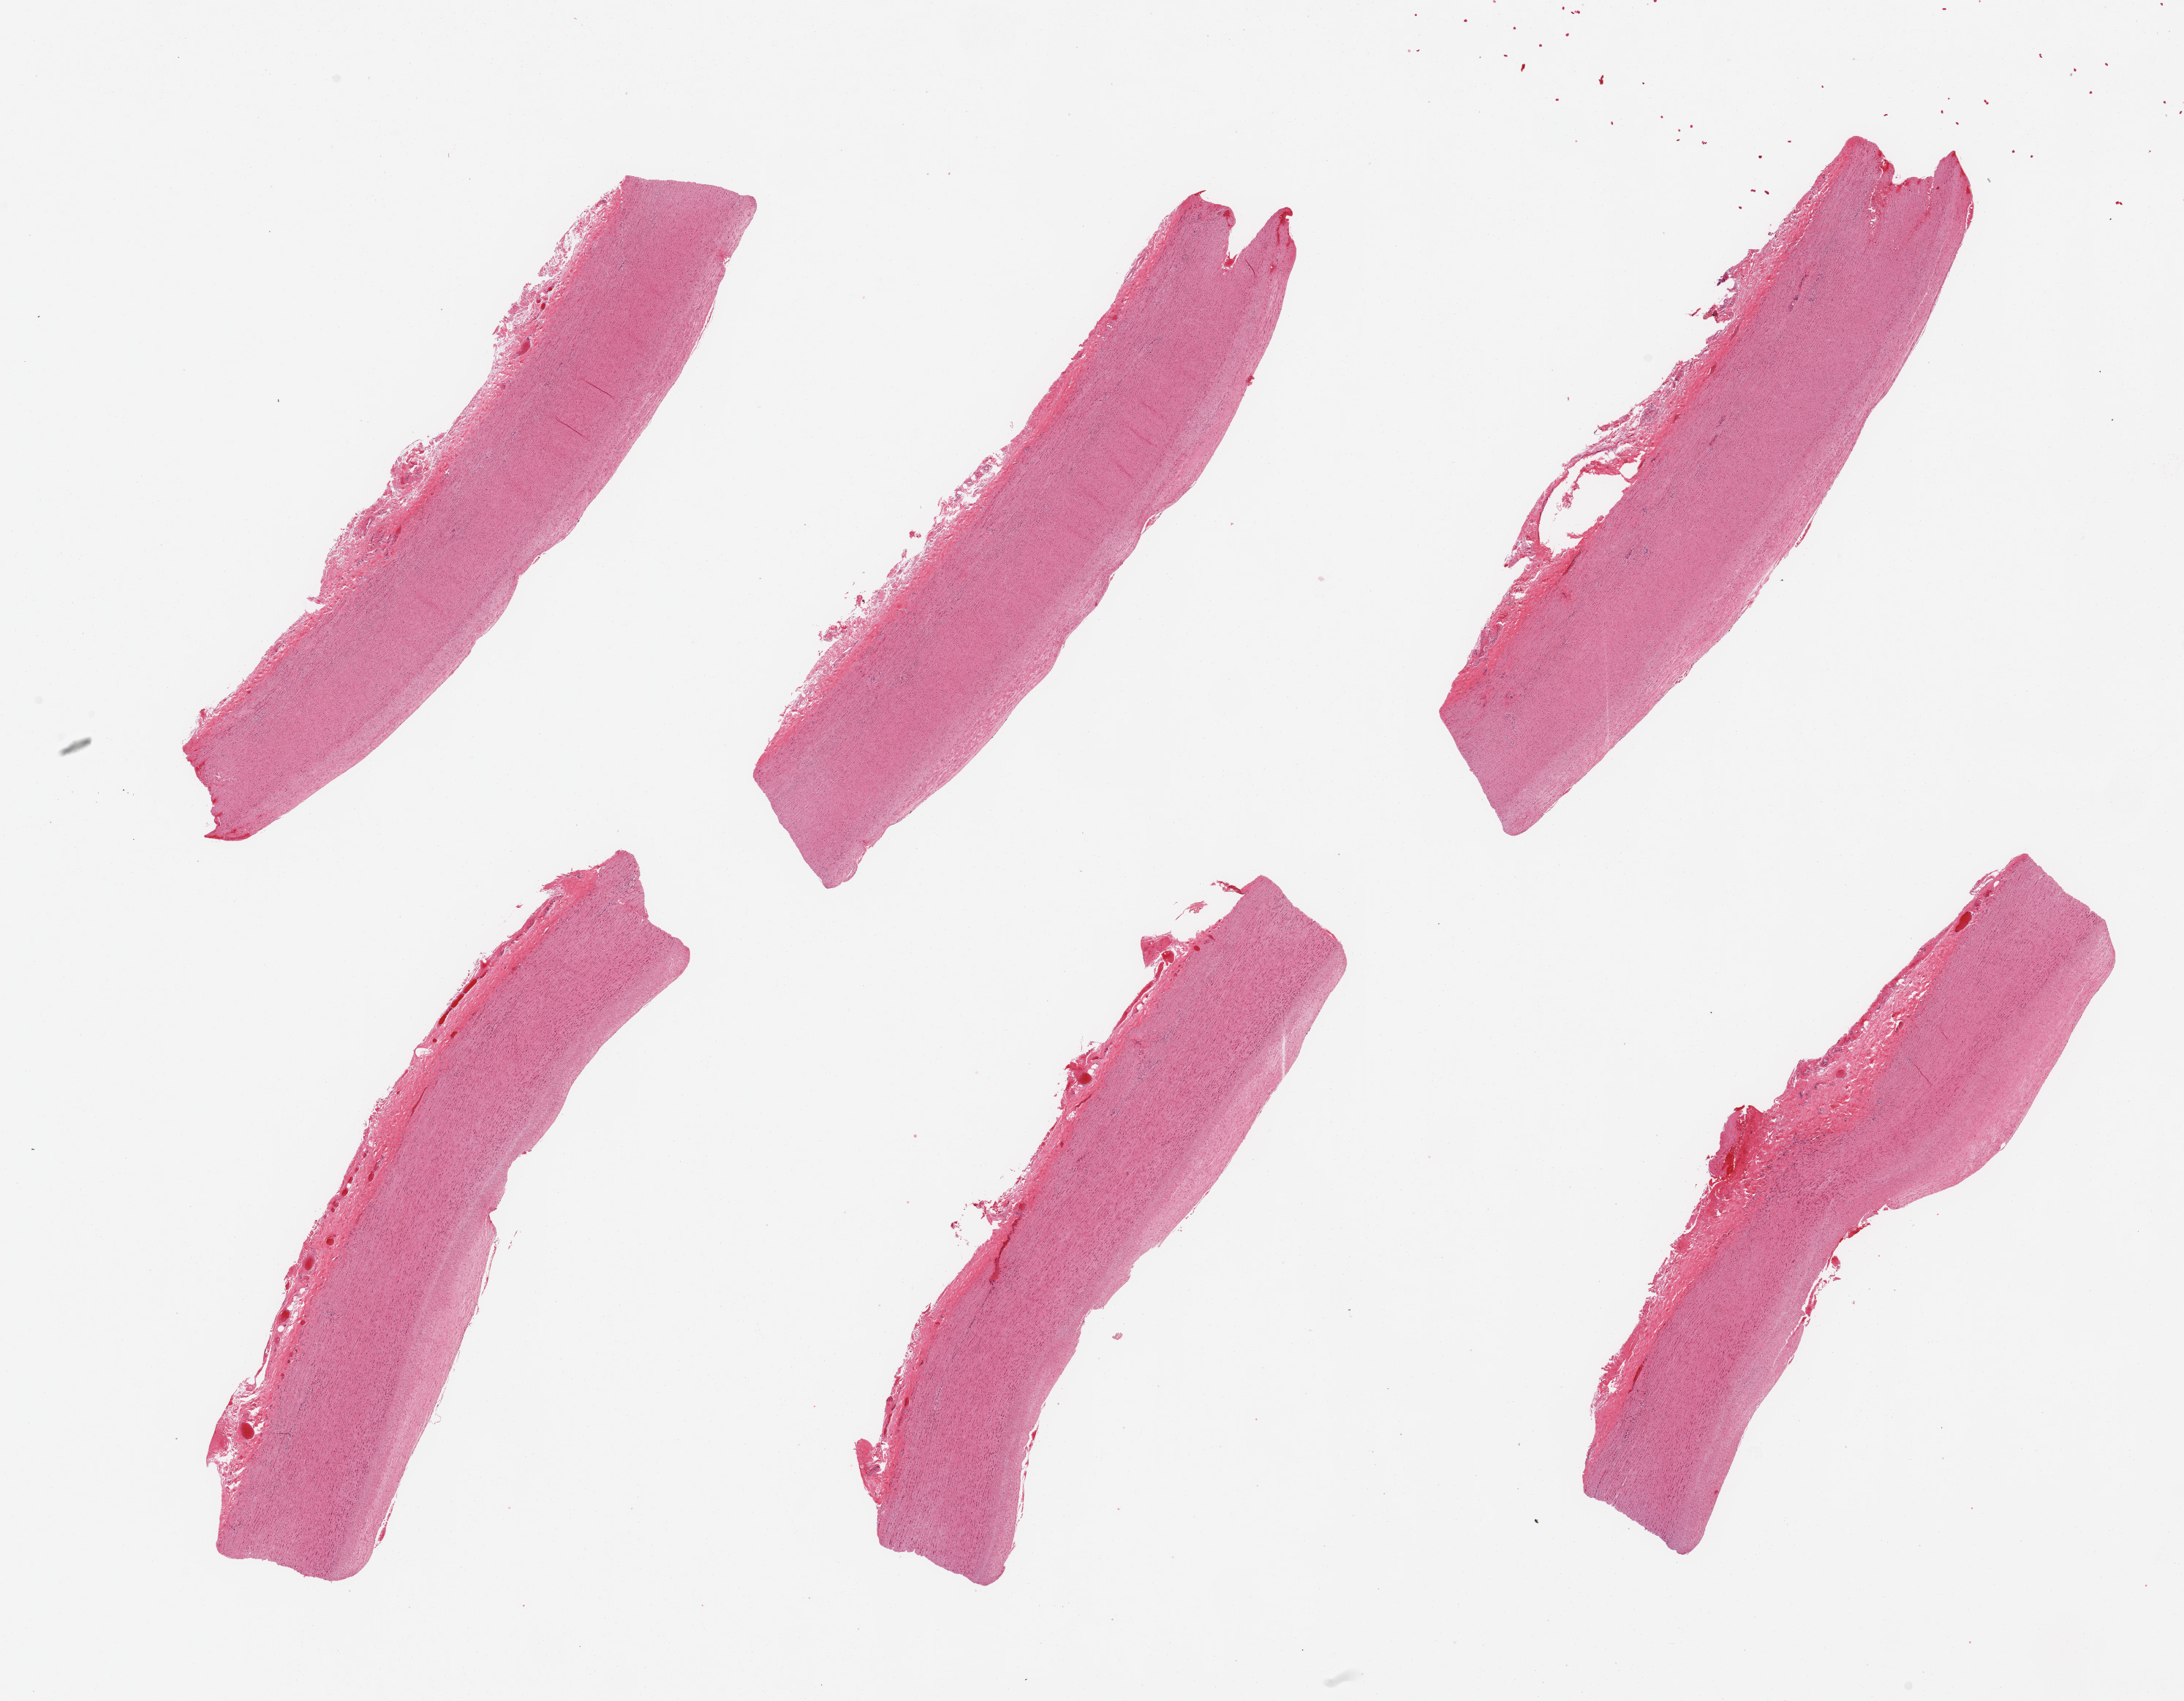
Digitized hematoxylin and eosin (H&E)-stained section — whole scanned area (about 23.6 x 18.4 mm) shown as a low-resolution overview. PAXgene-fixed, paraffin-embedded tissue. Target tissue: aorta. Tissue donor sample. Donor: male.
Review note (as recorded): 6 pieces; thin flat intimal fibrous plaques.